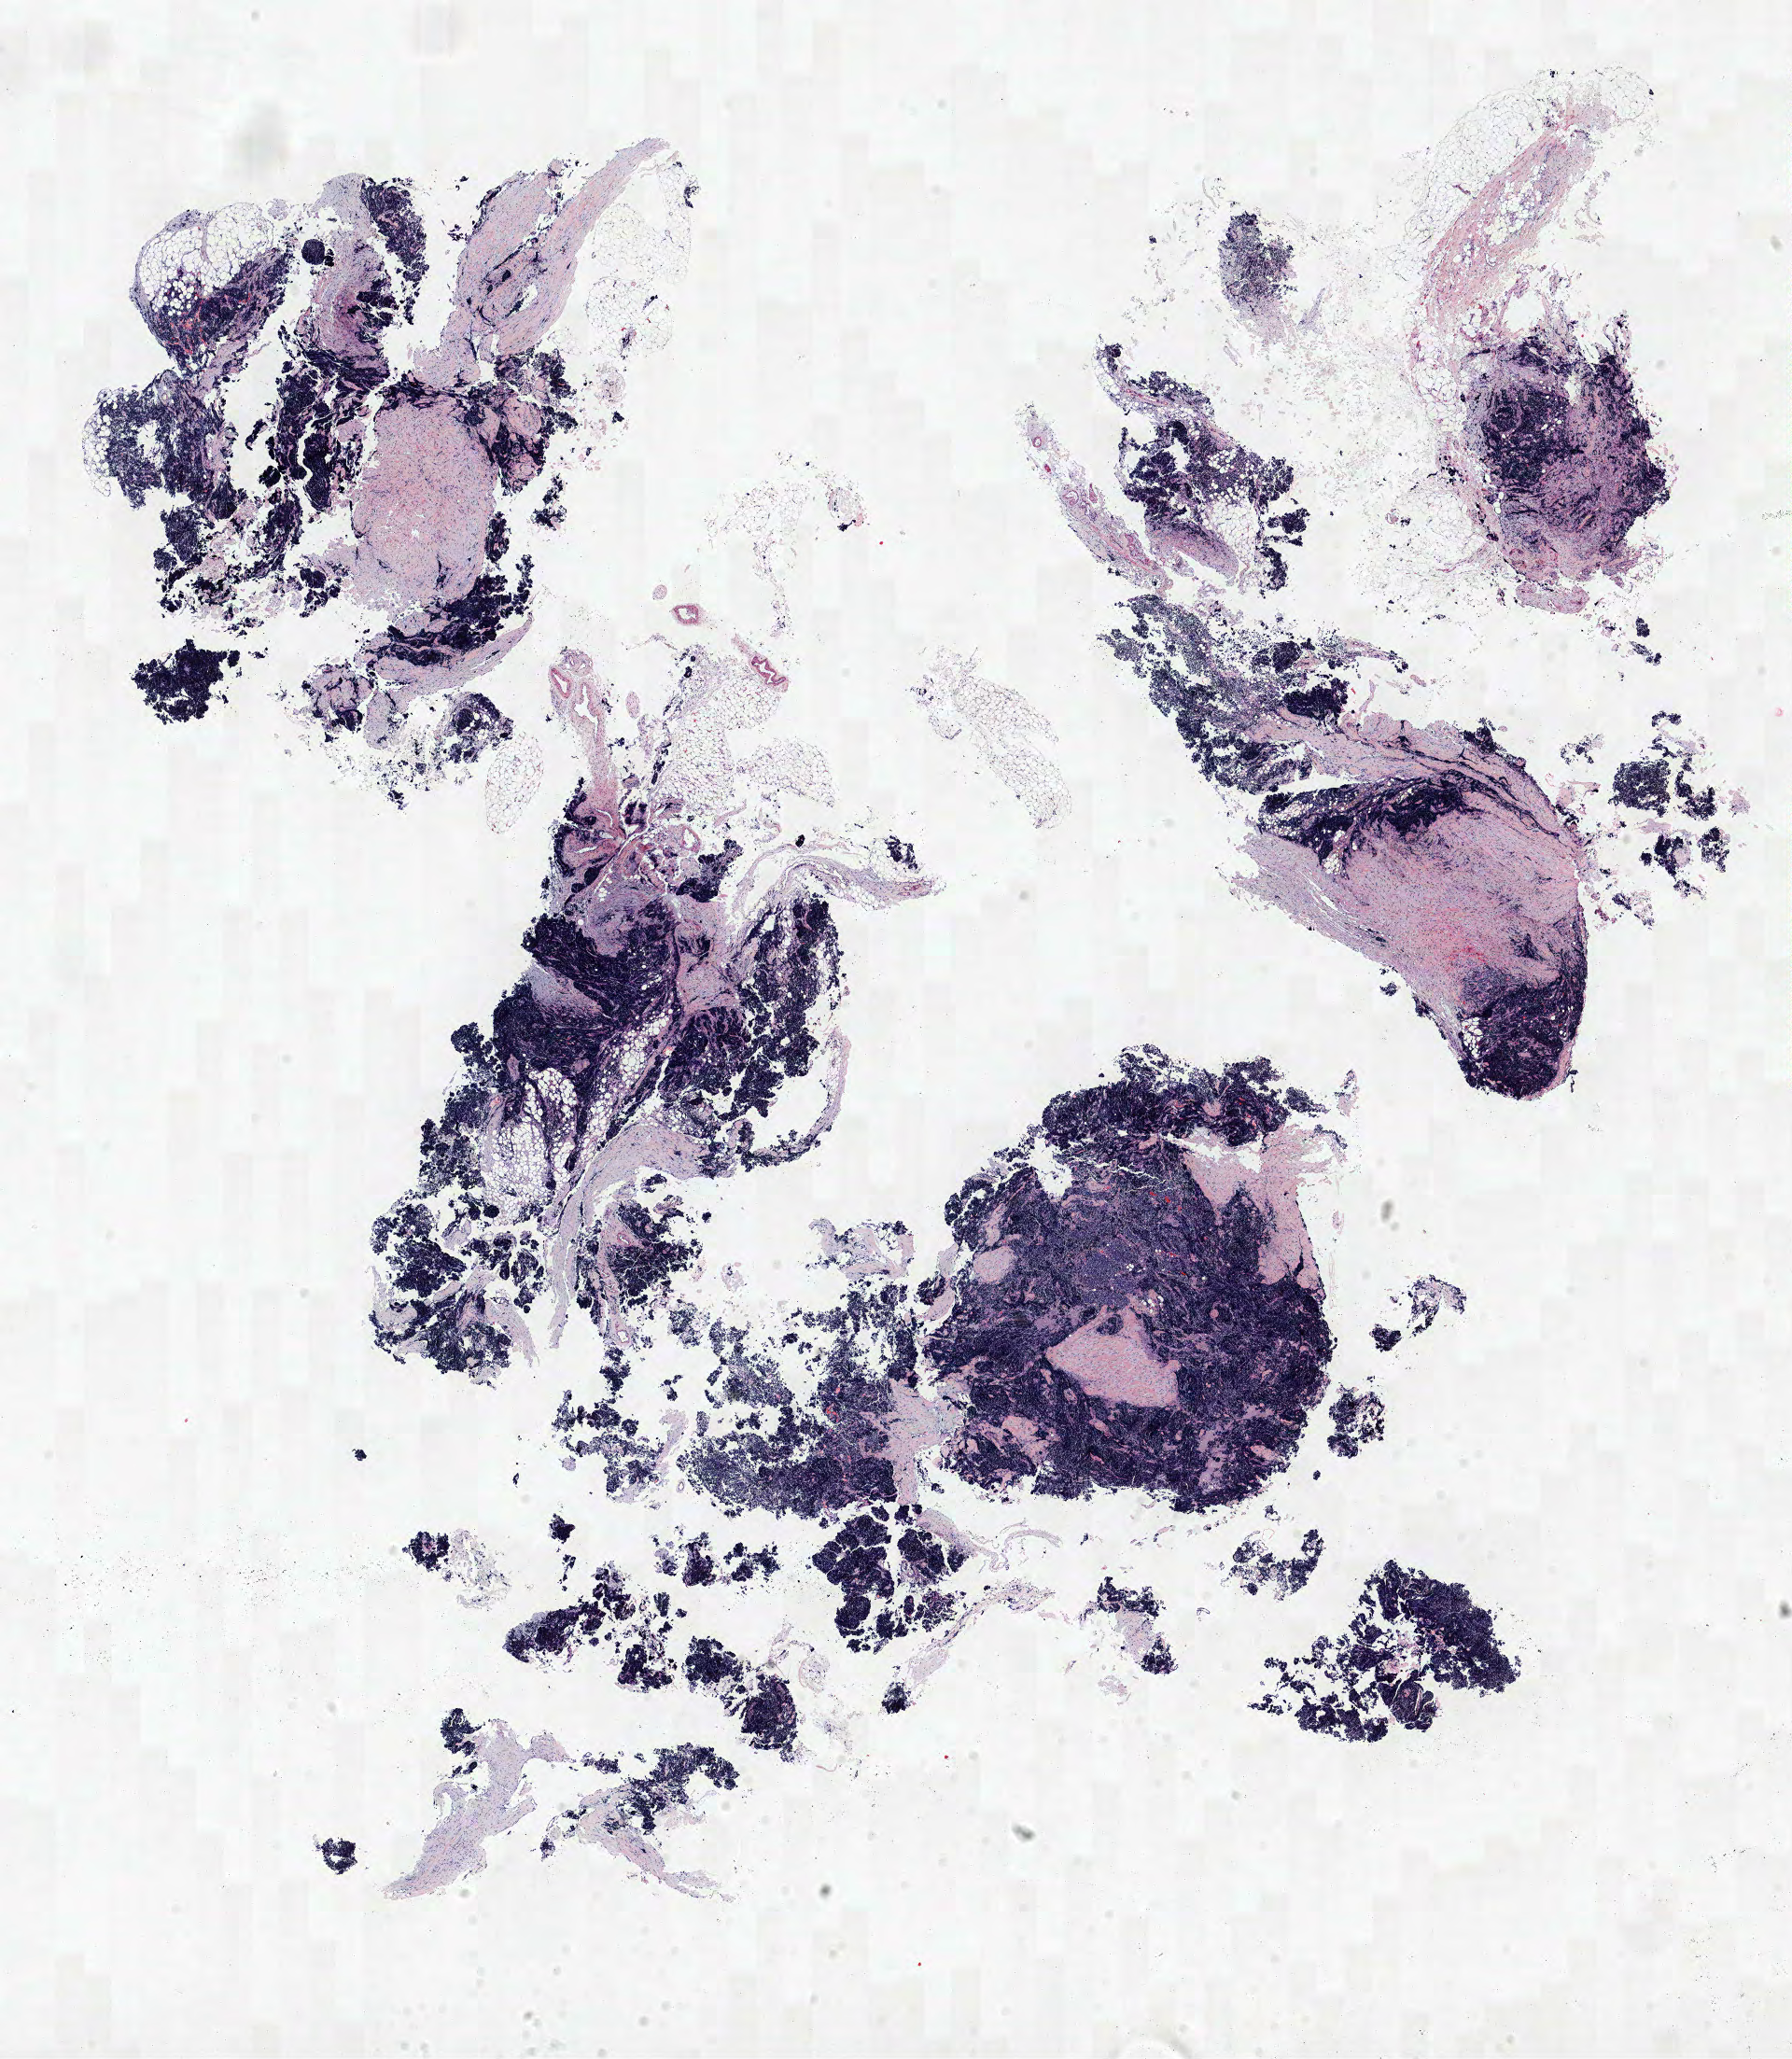
H&E whole-slide image — whole scanned area (about 15.4 x 17.7 mm) shown as a low-resolution overview. FFPE section. Lung. Female patient, aged 56 at enrolment. Former smoker at enrolment.
Participant's lung-cancer diagnosis: Small cell carcinoma, NOS (ICD-O-3 8041/3).